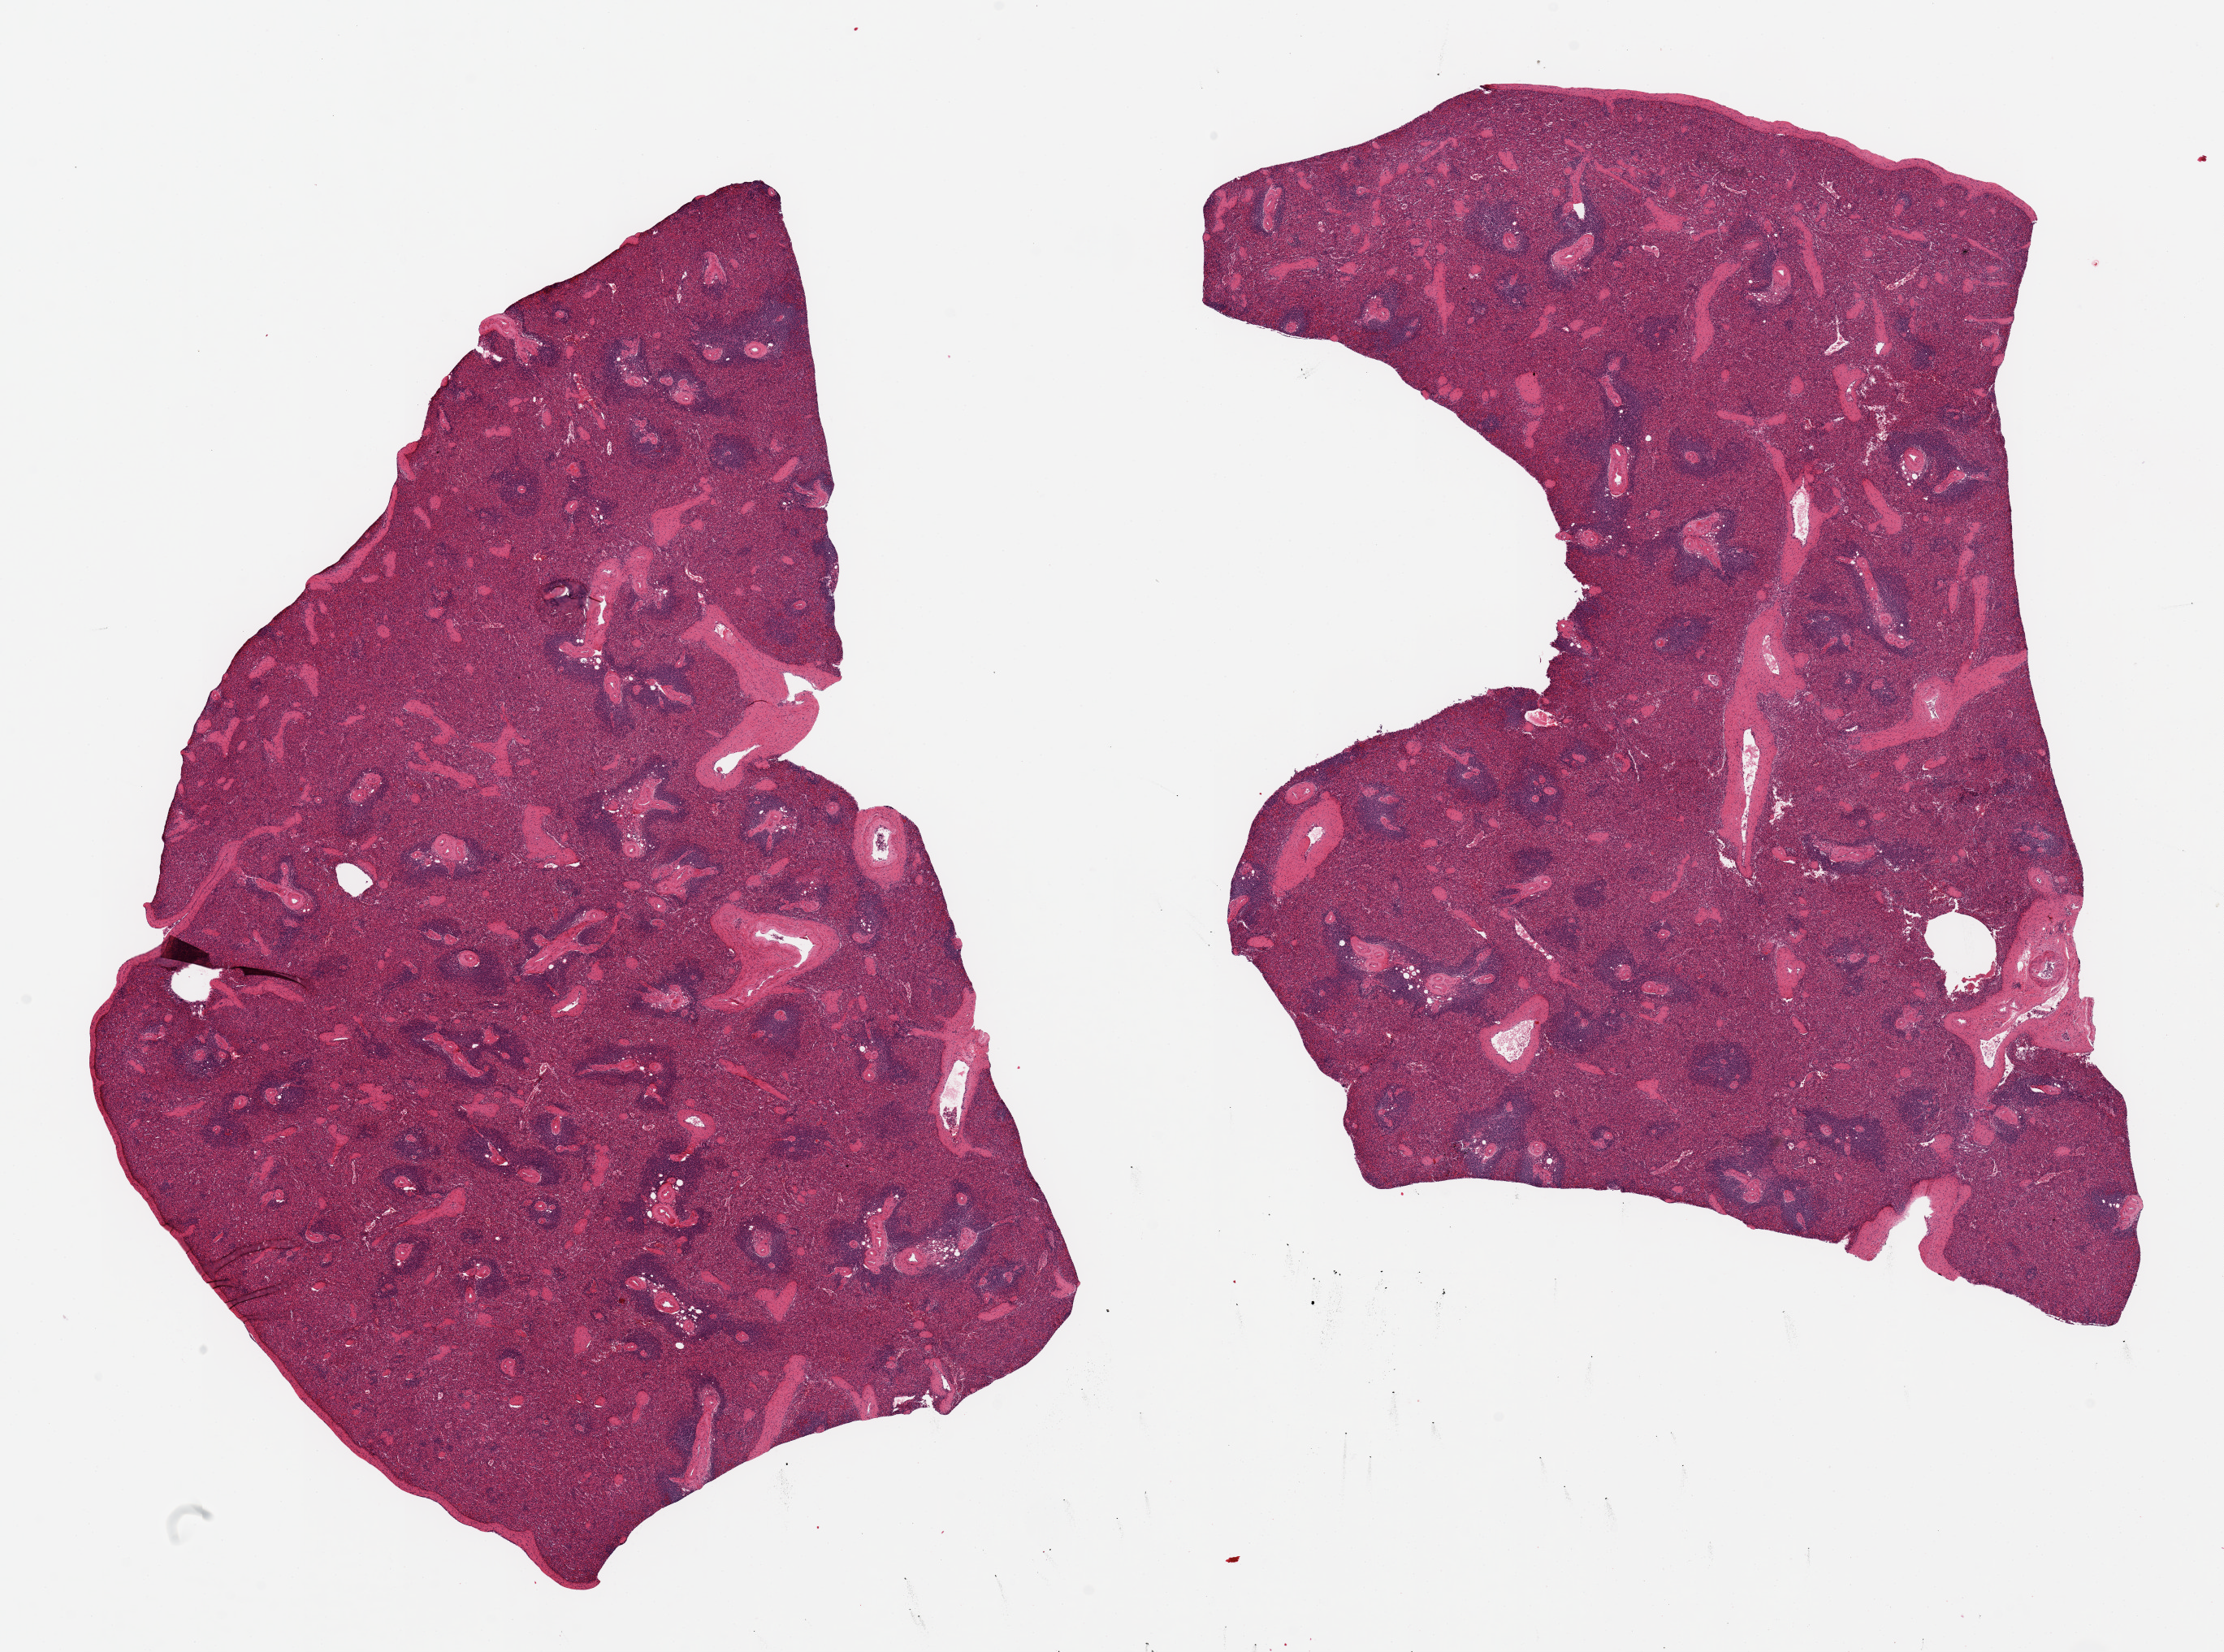
Digitized H&E-stained section — a low-resolution overview of the entire scanned area, about 21.7 x 16.1 mm (slide scanned at 20x). PAXgene-fixed, paraffin-embedded tissue. Sampled site (target tissue): spleen. Tissue donor sample.
Pathologist's review note for this sample: 2 pieces 12x8 & 11x8 mm.